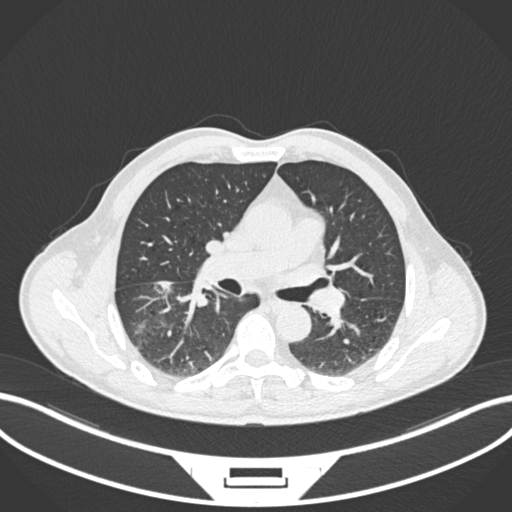
Chest CT, one axial slice. Position 113 of 208 along the scan axis. Reconstruction kernel B30f. 120 kVp. Lung window (W 1500 / L -600 HU). 512 × 512 image matrix, field of view 400 × 400 mm. Patient: male, 58 years. Case-level facts recorded for this patient, not image findings: clinical TNM (as recorded): T3 N0 M0; histopathological grade: G2.
Annotated regions visible in this slice (bounding box drawn by a radiologist):
- lung tumour (recorded histology: squamous cell carcinoma): bounding box <154,278,176,294> (left, top, right, bottom; pixels)